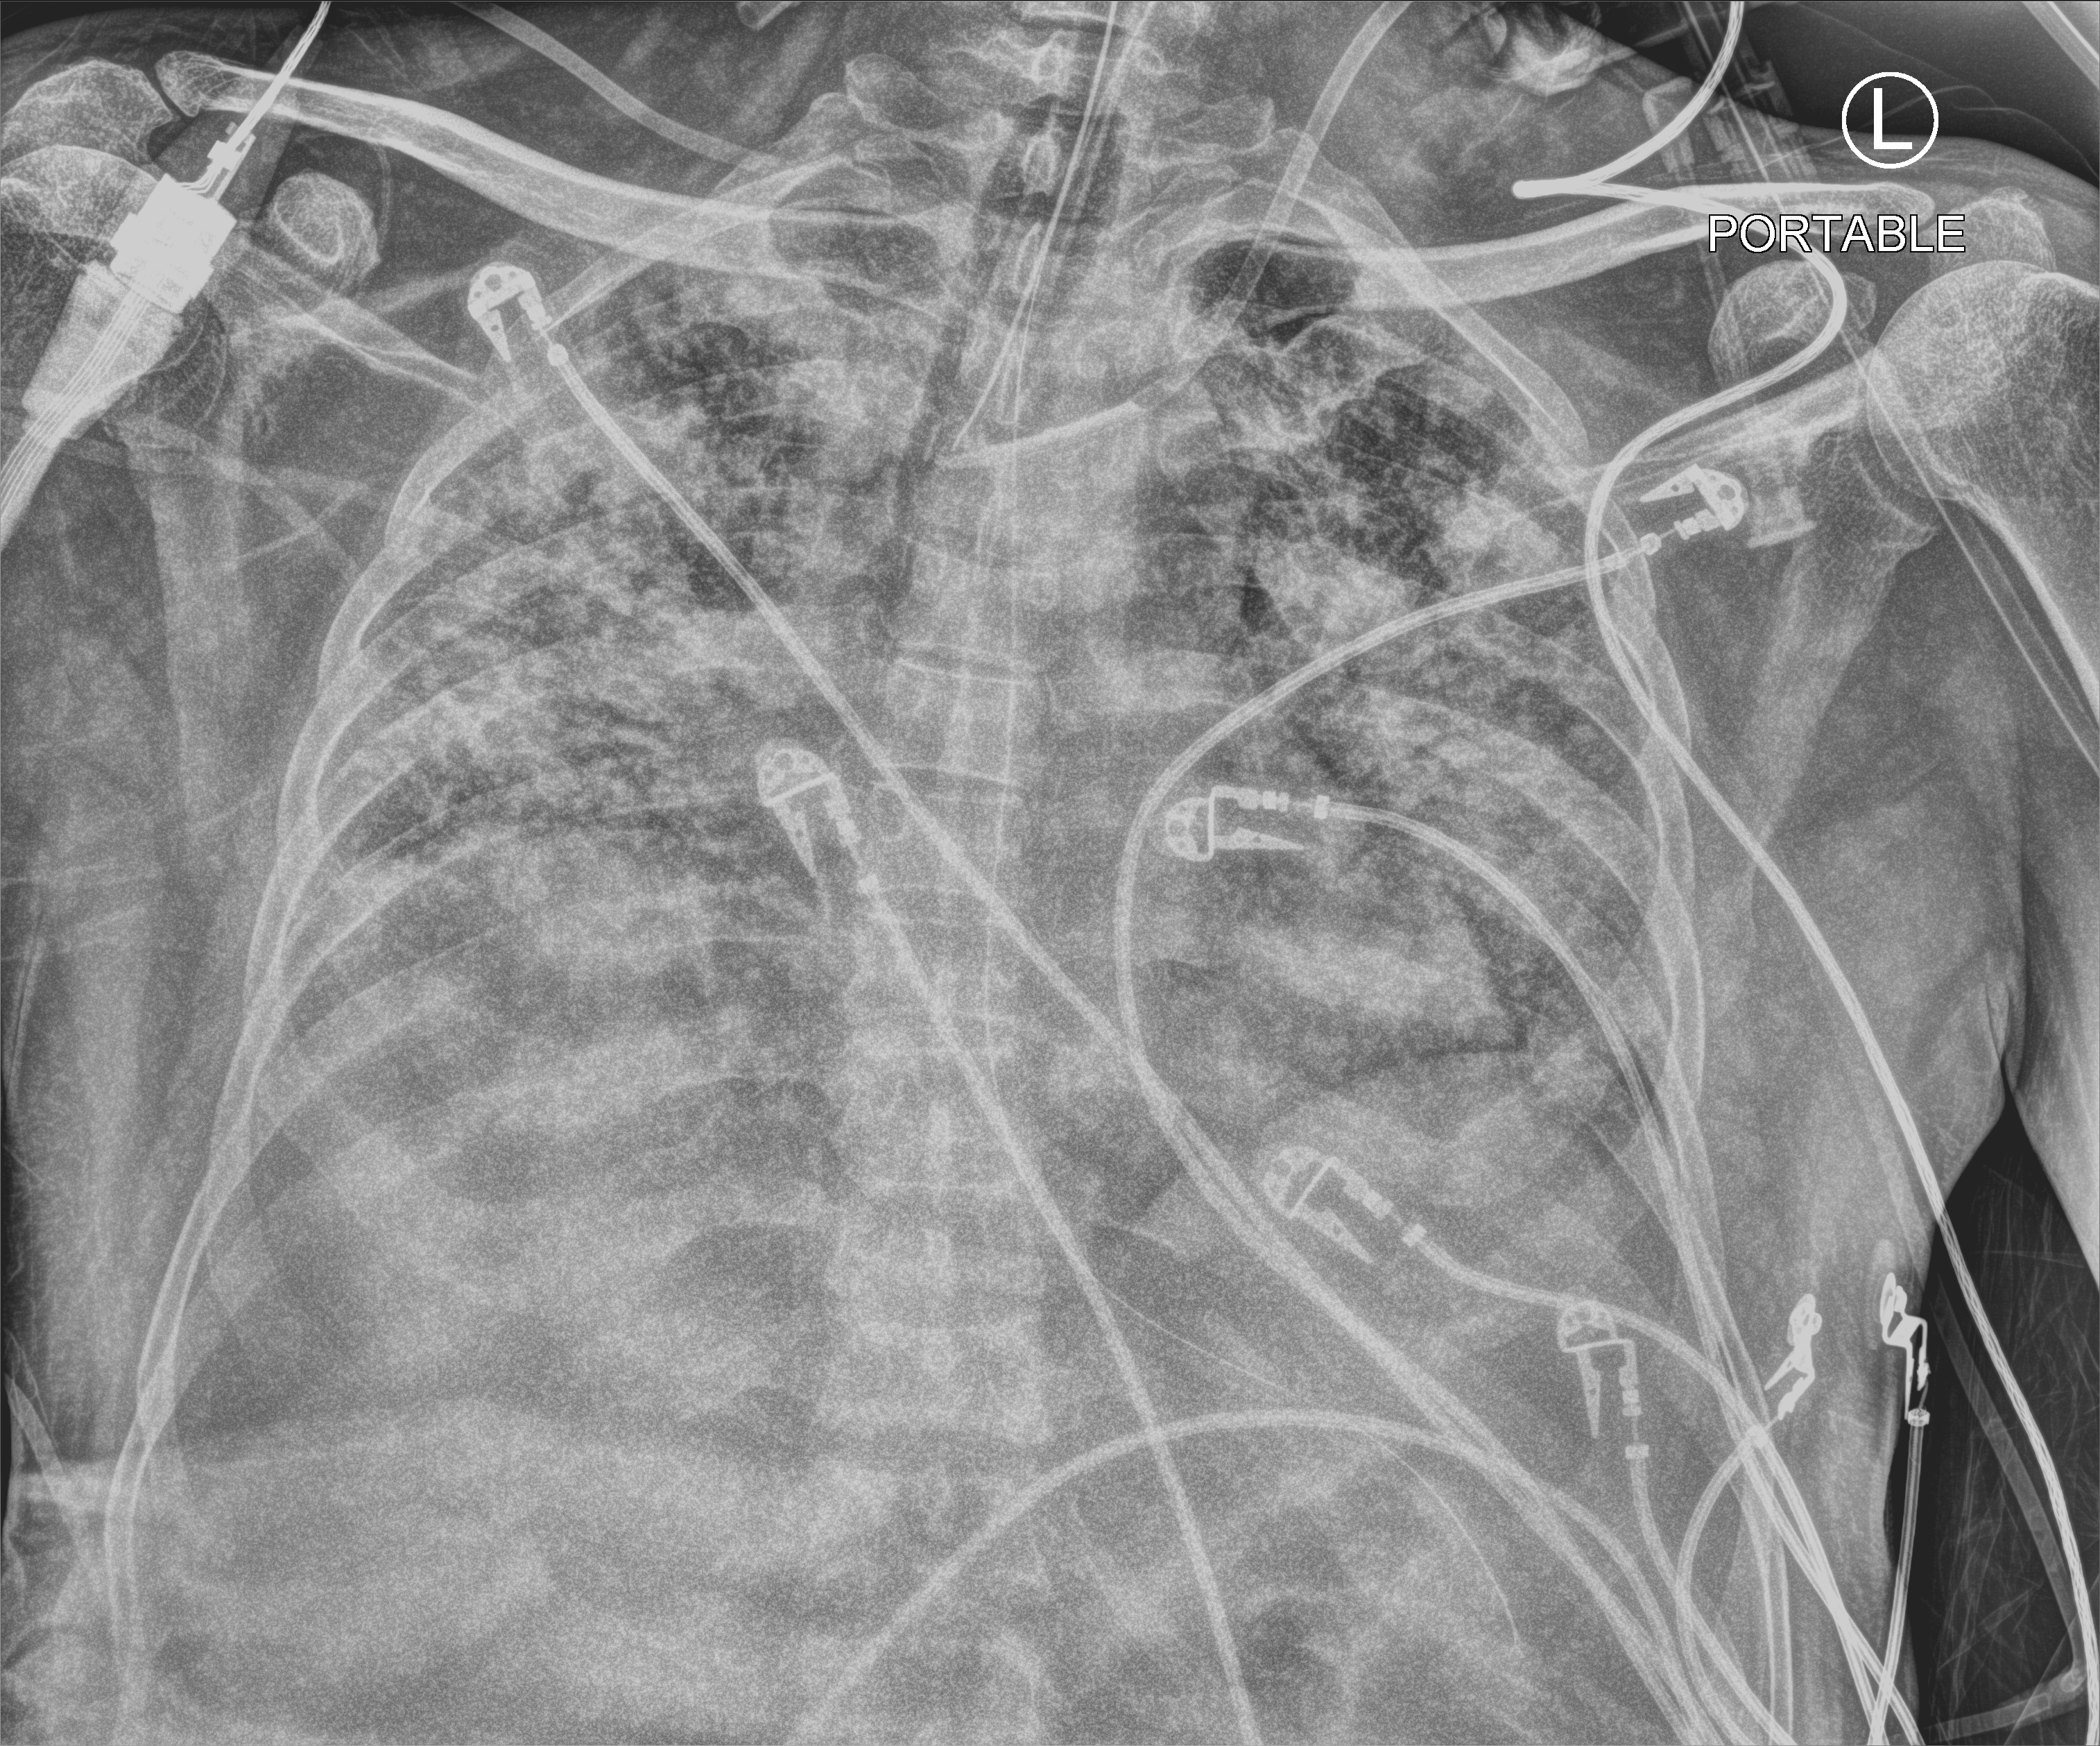
Chest X-ray (portable); anteroposterior (AP) projection. Patient hospitalised with COVID-19; male, aged 60–74 years.
From the hospital-stay record, not from the radiograph (when in the stay this image was taken is not recorded): admitted to intensive care during this hospital stay: yes; mechanically ventilated during this hospital stay: yes.